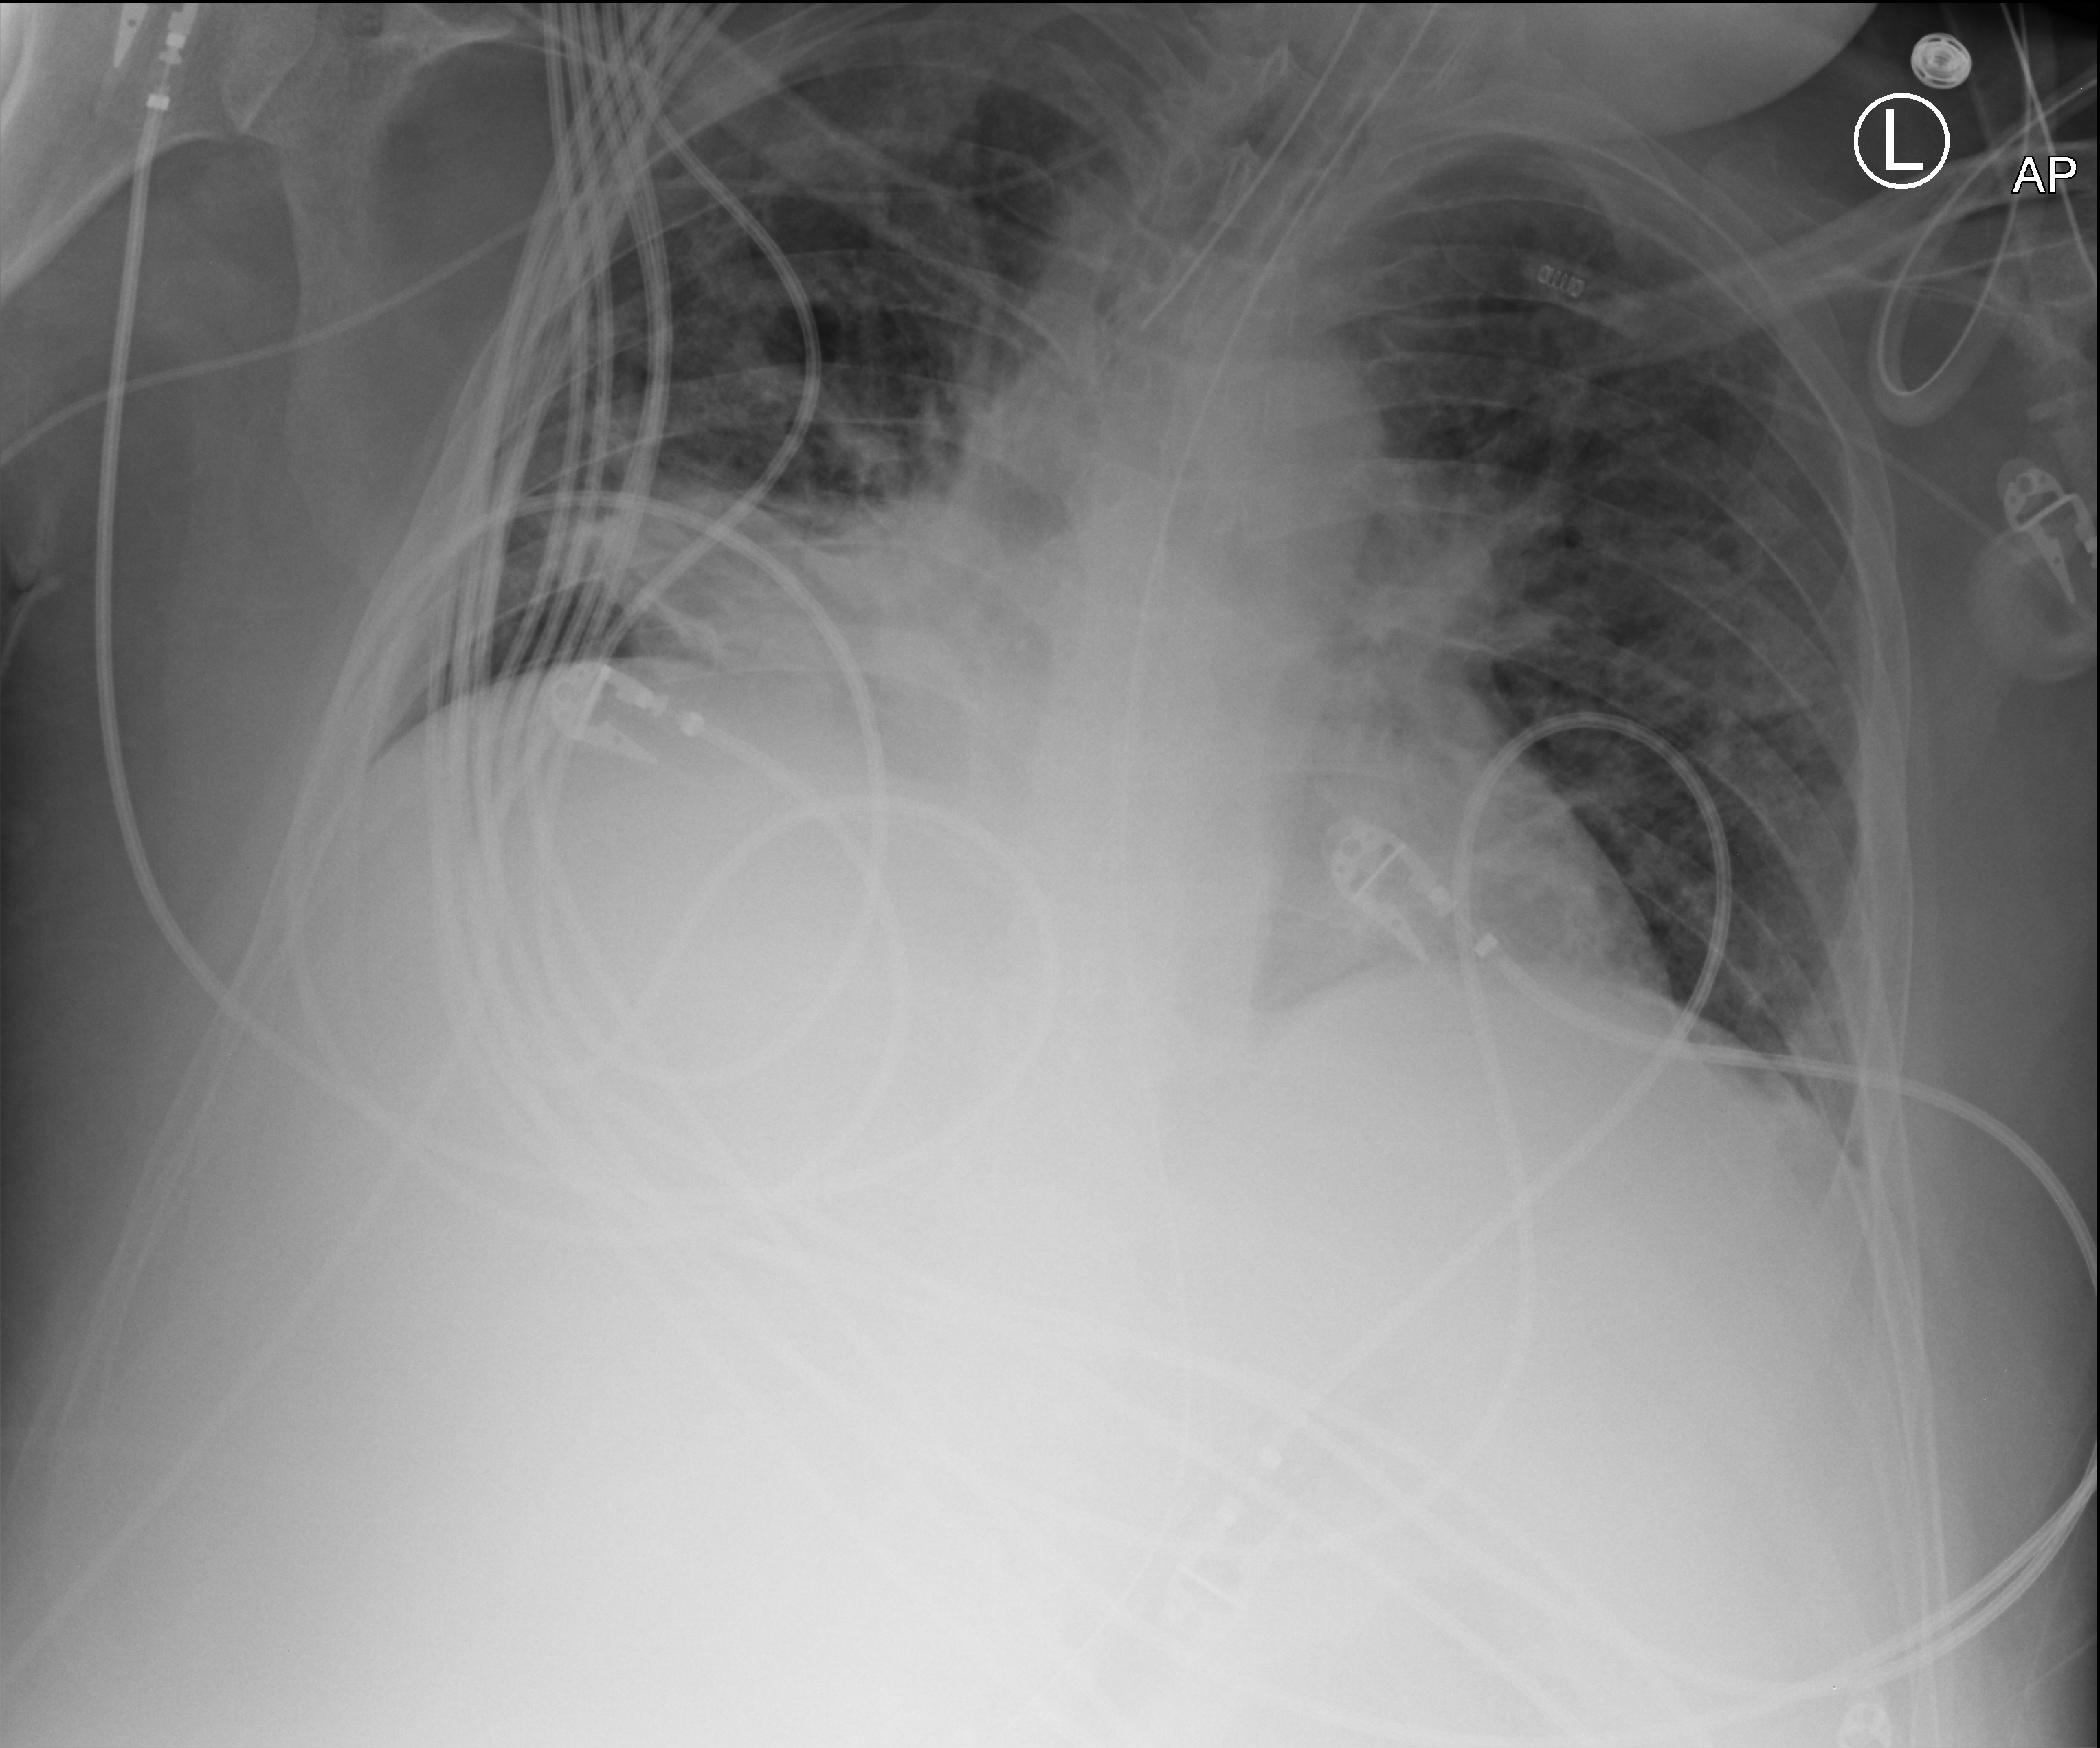
Chest X-ray (portable). Patient hospitalised with COVID-19, aged 18–59 years.
Admission-level facts for this patient (not findings on this image; timing relative to this image not recorded): length of hospital stay: 50 days; admitted to intensive care during this hospital stay: yes.